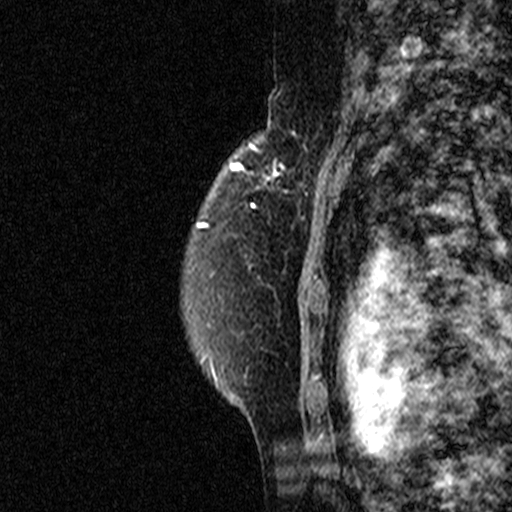
Breast MRI (dynamic contrast-enhanced), one sagittal slice; slice 33 of 44 in the series (ordered by position); dynamic contrast-enhanced study with each time point stored as its own series, time point 2 of 3 at this slice position (early post-contrast, ordered by acquisition time); 1.5 T; TE 4.5 ms, TR 11 ms; 3 mm slice thickness; 512 × 512 image matrix. Patient: female, 49 years. From the clinical record (not read from this slice): setting: breast cancer imaged before/during neoadjuvant chemotherapy; receptor status: triple-negative.
Structures marked on this image (semi-automatic segmentation, software-assisted and operator-edited):
- analysis volume of interest (the breast-tissue region the enhancement analysis was run in; not a lesion): box from (x=262, y=122) to (x=331, y=227) px
- tumour enhancement mask (voxels above the 90 % enhancement threshold inside the analysis volume of interest): (x=265, y=163)–(x=302, y=192)